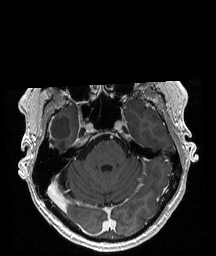
Brain MRI from a brain-tumour surgery series, one axial slice; slice 139 of 208 in the series (ordered by position); T1-weighted post-contrast; 216 × 256 image matrix, field of view 211 × 250 mm. From the clinical record (not read from this slice): histopathology: Astrocytoma; WHO grade: 4; IDH mutation: yes.
Outlined on this slice (outlined manually by an expert reader):
- tumour: bounding box (x1, y1, x2, y2) in pixels: (50, 146, 52, 148)